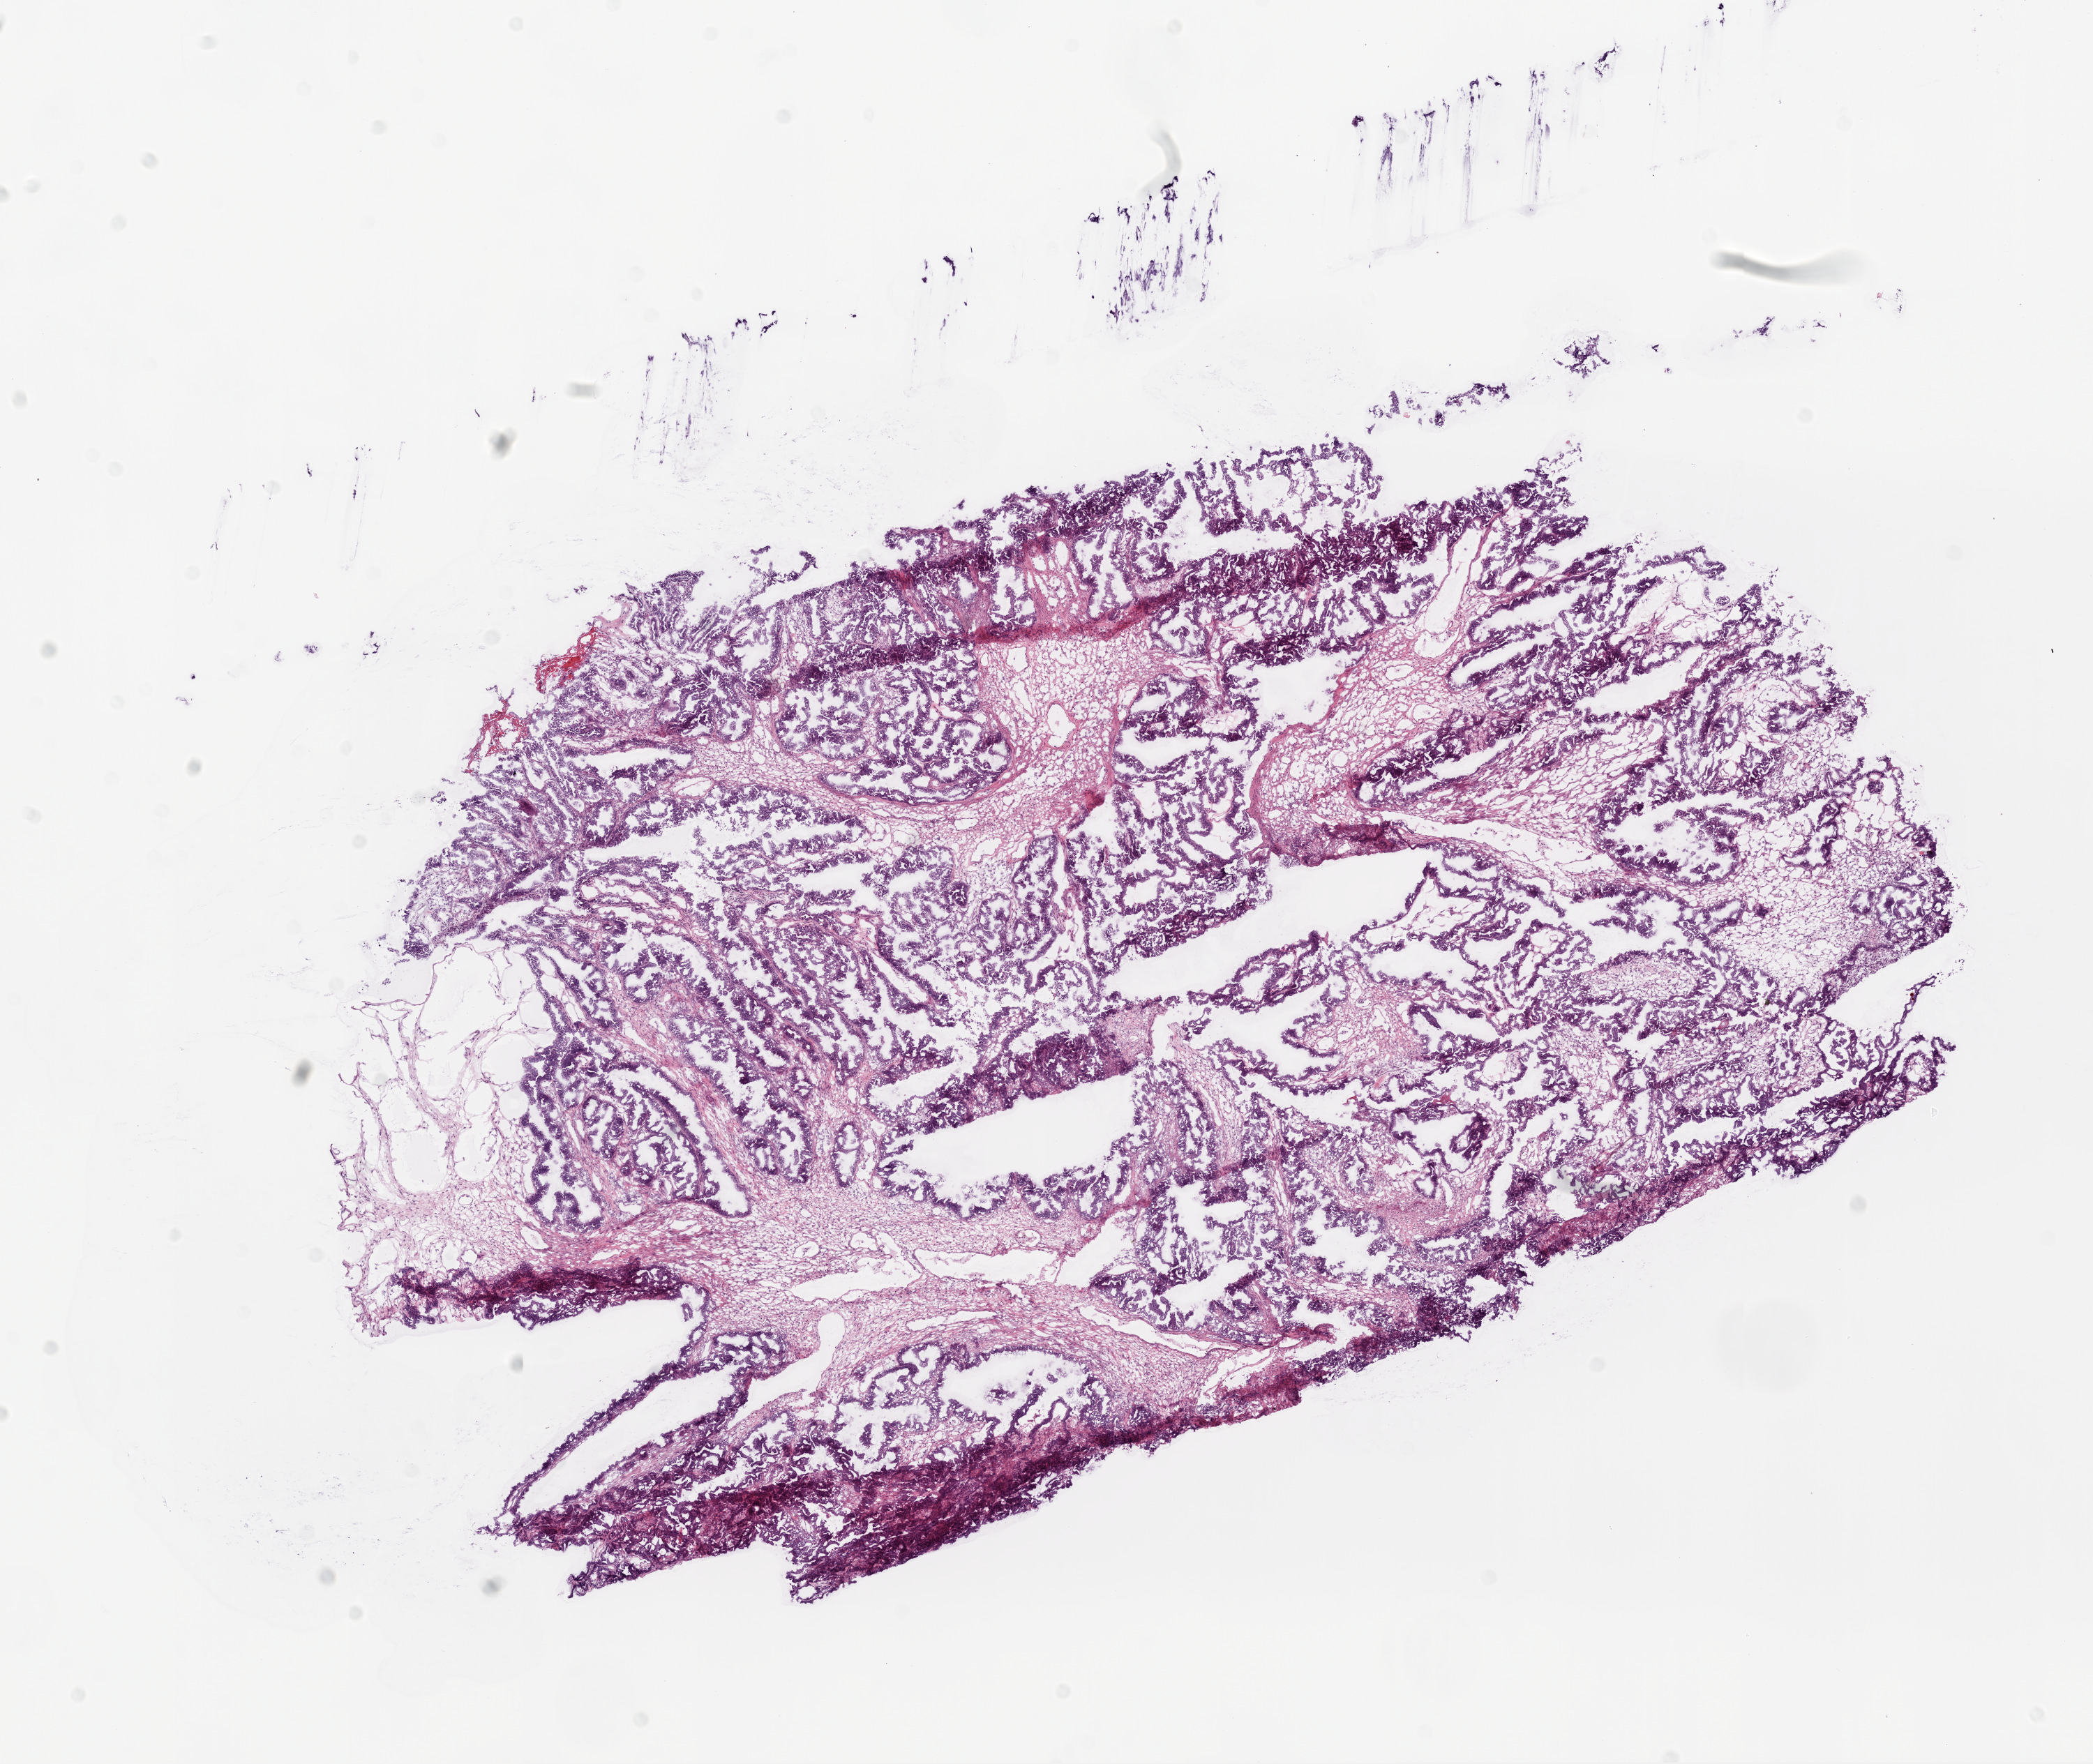
H&E-stained whole-slide image, whole scanned area (about 12.0 x 10.1 mm) shown as a low-resolution overview, frozen section from the bottom of the tissue portion, sample: primary tumour, ovary. Female patient; age at initial diagnosis 58 years. Composition of this section per pathologist review: tumour cells 70%, tumour nuclei 75%.
Pathologic diagnosis: Serous cystadenocarcinoma, NOS.